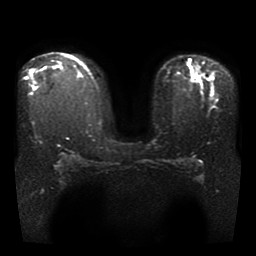
Breast MRI, one axial slice; slice 24 of 37 in the series (ordered by position); diffusion-weighted series; image 2 of 4 stored at this slice position (different b-values; order by instance number); 1.5 T; 256 × 256 image matrix, field of view 330 × 330 mm. Female patient.
Structures marked on this image (expert manual segmentation):
- tumour on diffusion-weighted imaging: bounding box <189,66,196,76> (left, top, right, bottom; pixels)